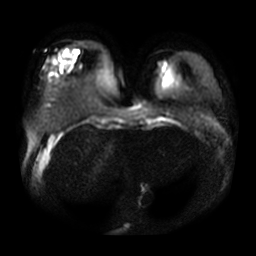
Breast MRI, one axial slice. Slice 8 of 29 in the series (ordered by position). Diffusion-weighted series; image 2 of 4 stored at this slice position (different b-values; order by instance number). 3 T. 256 × 256 image matrix. Female patient.
Structures marked on this image (expert manual segmentation):
- tumour on diffusion-weighted imaging: bounding box <63,53,69,68> (left, top, right, bottom; pixels)